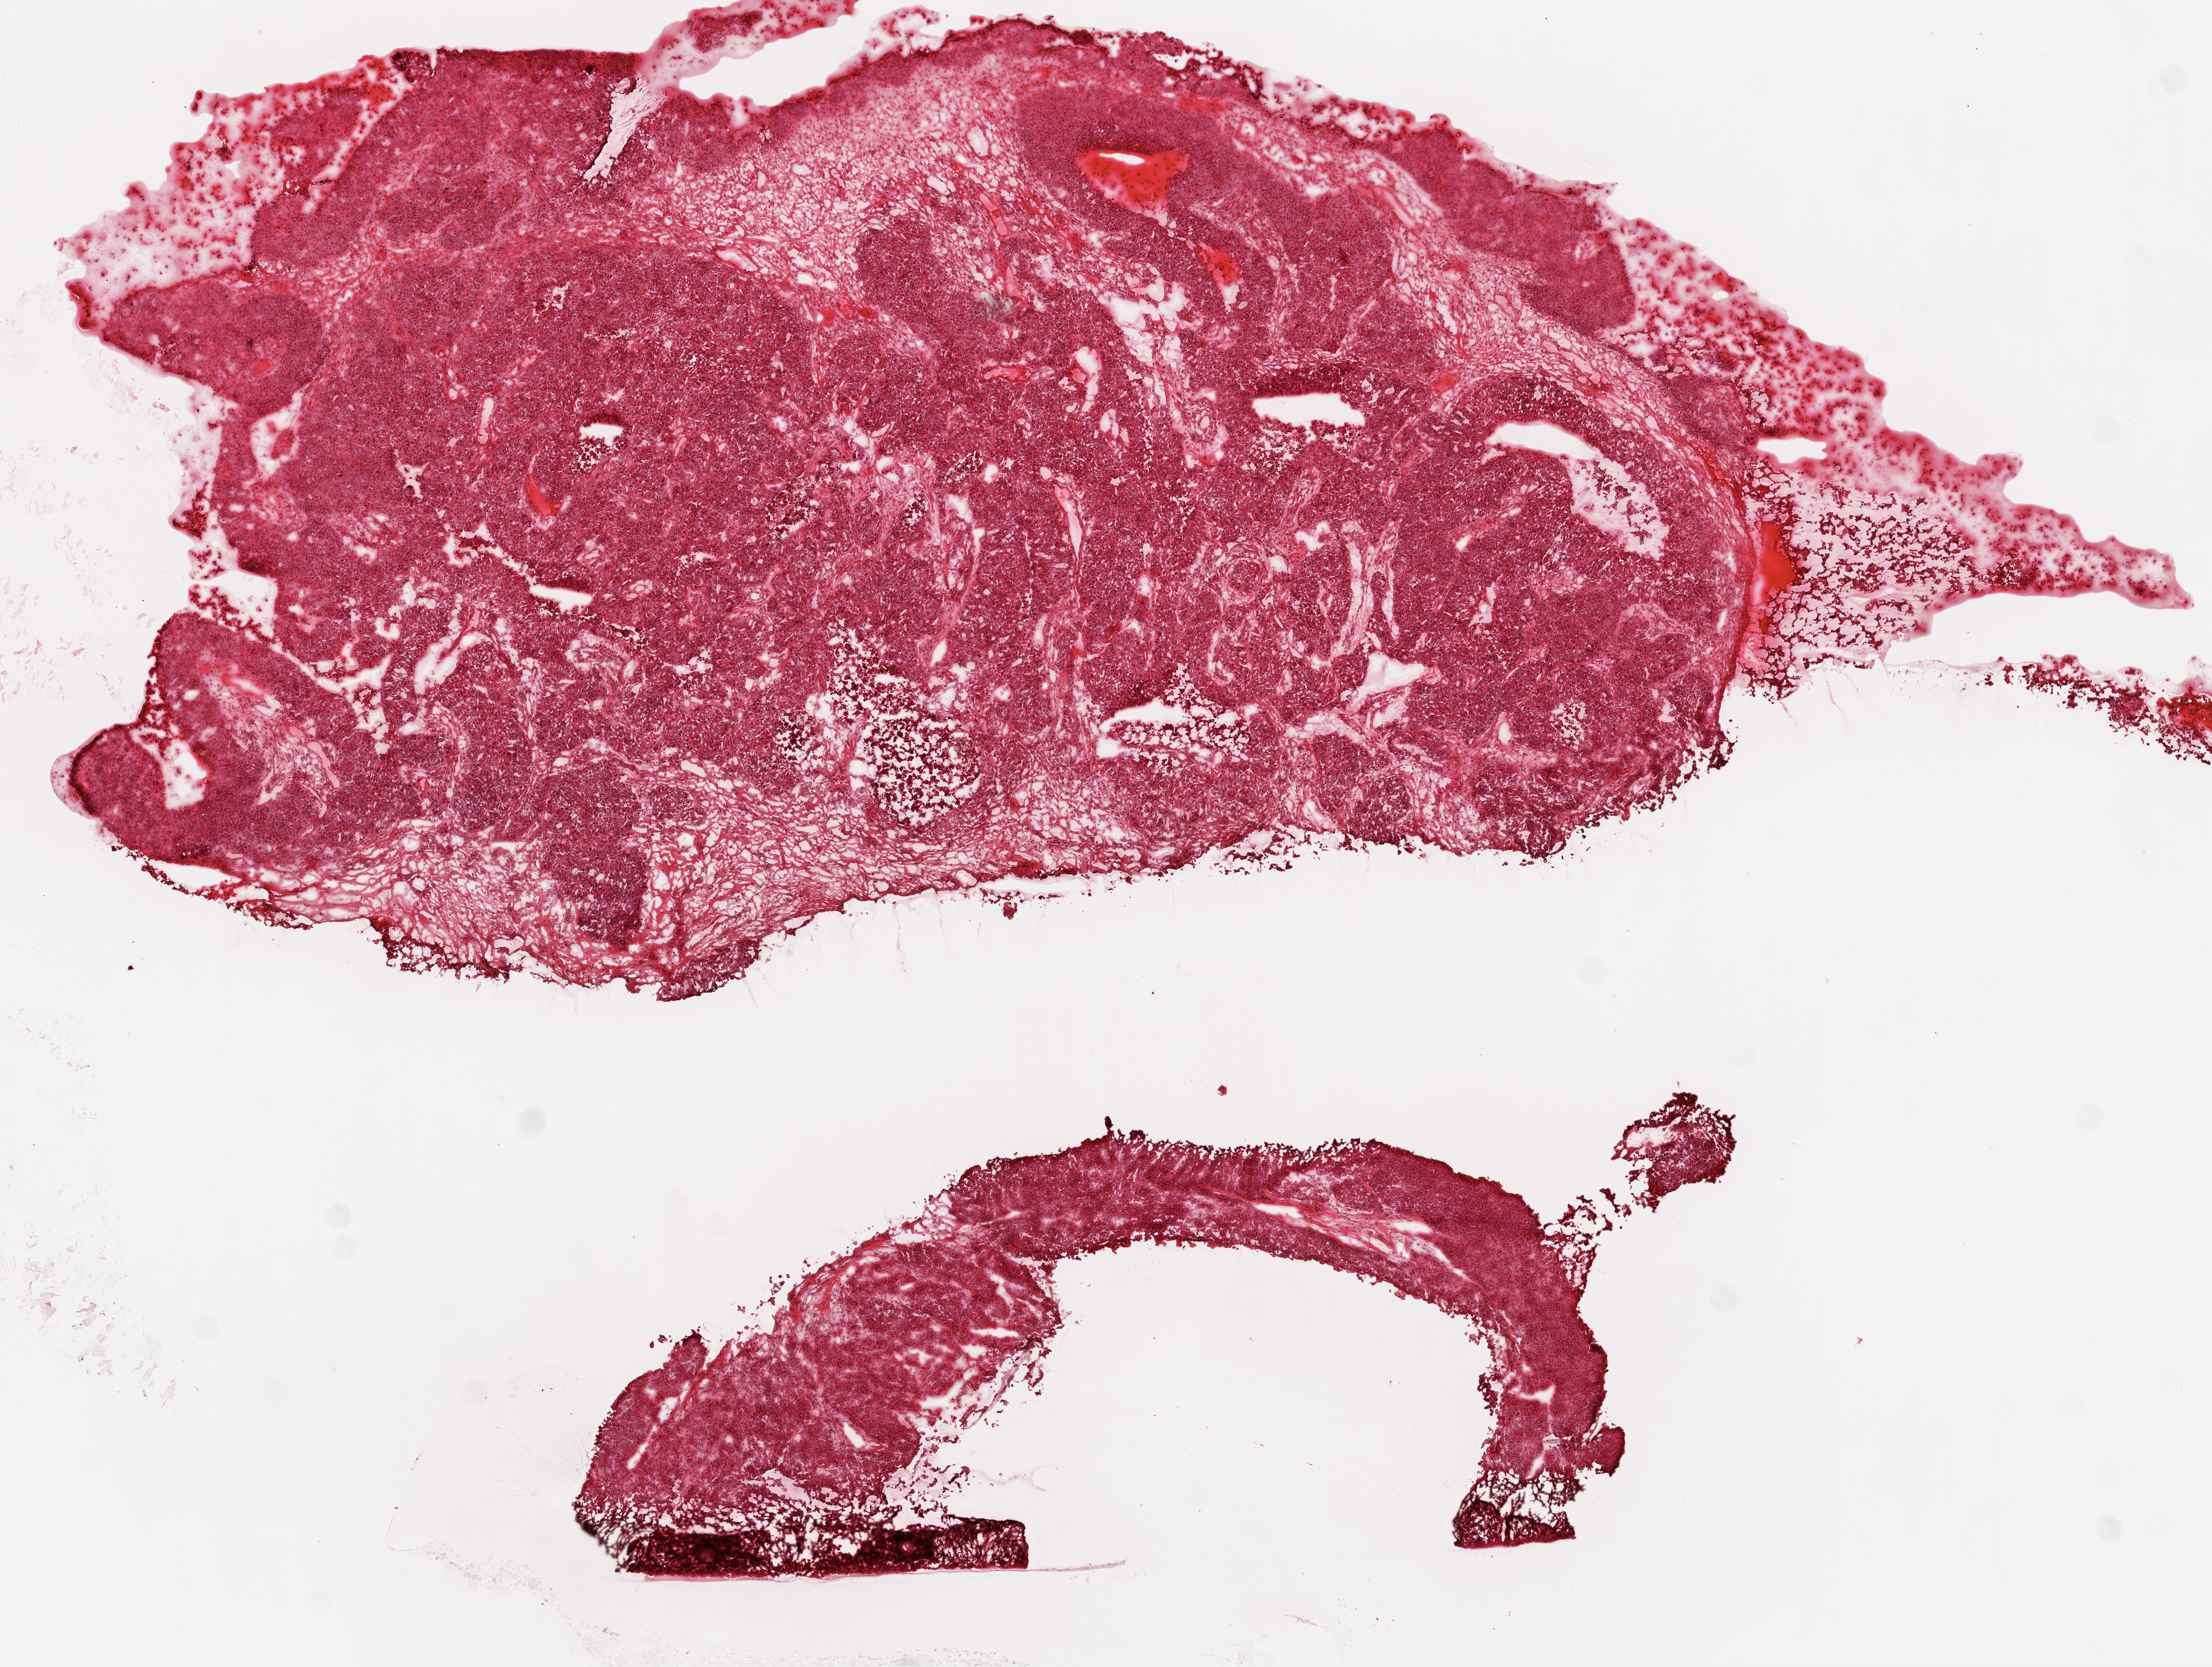
Hematoxylin and eosin (H&E) stained whole-slide image — low-resolution overview of the scanned area, about 10.0 x 7.6 mm (acquisition: 20x scan); frozen section from the top of the tissue portion; sample: primary tumour, ovary. Female, age 58 years at initial diagnosis. Histologic grade: G3 (poorly differentiated). Slide review estimates, as recorded: tumour cells 85%, tumour nuclei 95%, normal cells 0%, stromal cells 10%, necrosis 5%.
* FIGO stage: IIIB
* laterality: bilateral
* diagnosis: Serous cystadenocarcinoma, NOS